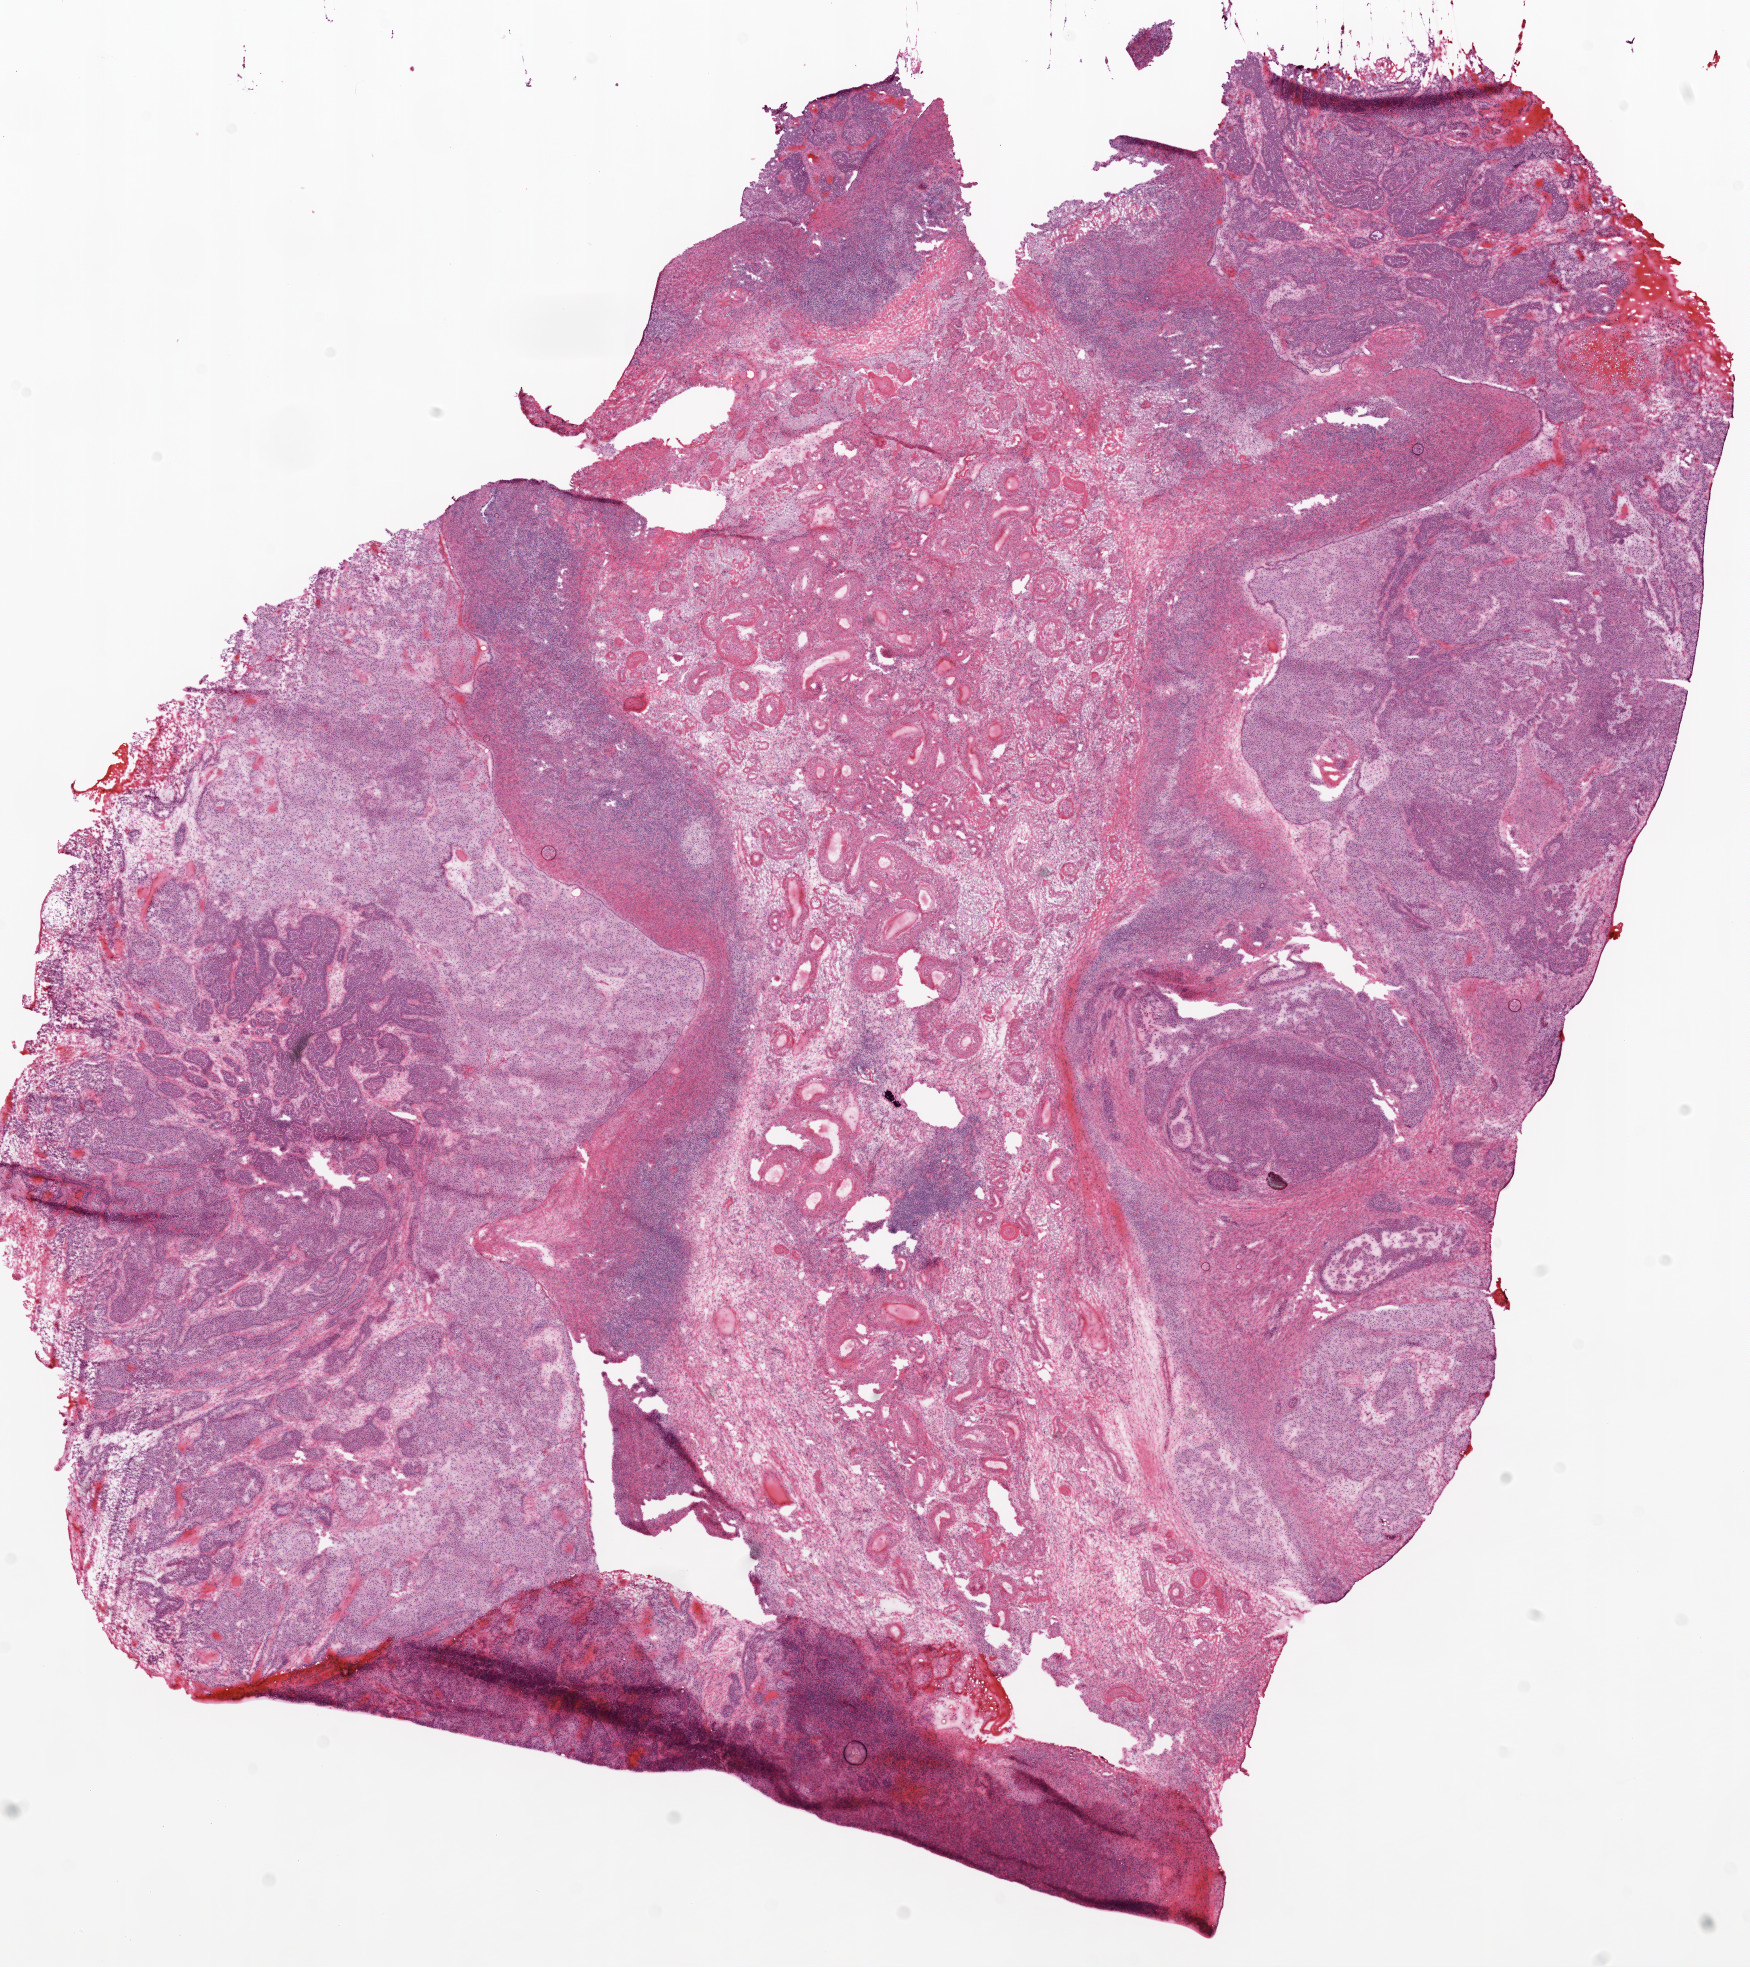
Whole-slide histology image, Hematoxylin and eosin (H&E) stained — low-resolution overview of the scanned area, about 14.0 x 15.8 mm, frozen section from the top of the tissue portion, primary tumour sample from the ovary. Patient: female, age at initial diagnosis 66 years. Histologic grade: G3 (poorly differentiated). Pathologist review of this section (percent, as recorded): tumour cells 60%, tumour nuclei 90%, normal cells 30%, stromal cells 5%, necrosis 5%.
* pathologic diagnosis: Serous cystadenocarcinoma, NOS
* FIGO stage: IIIC